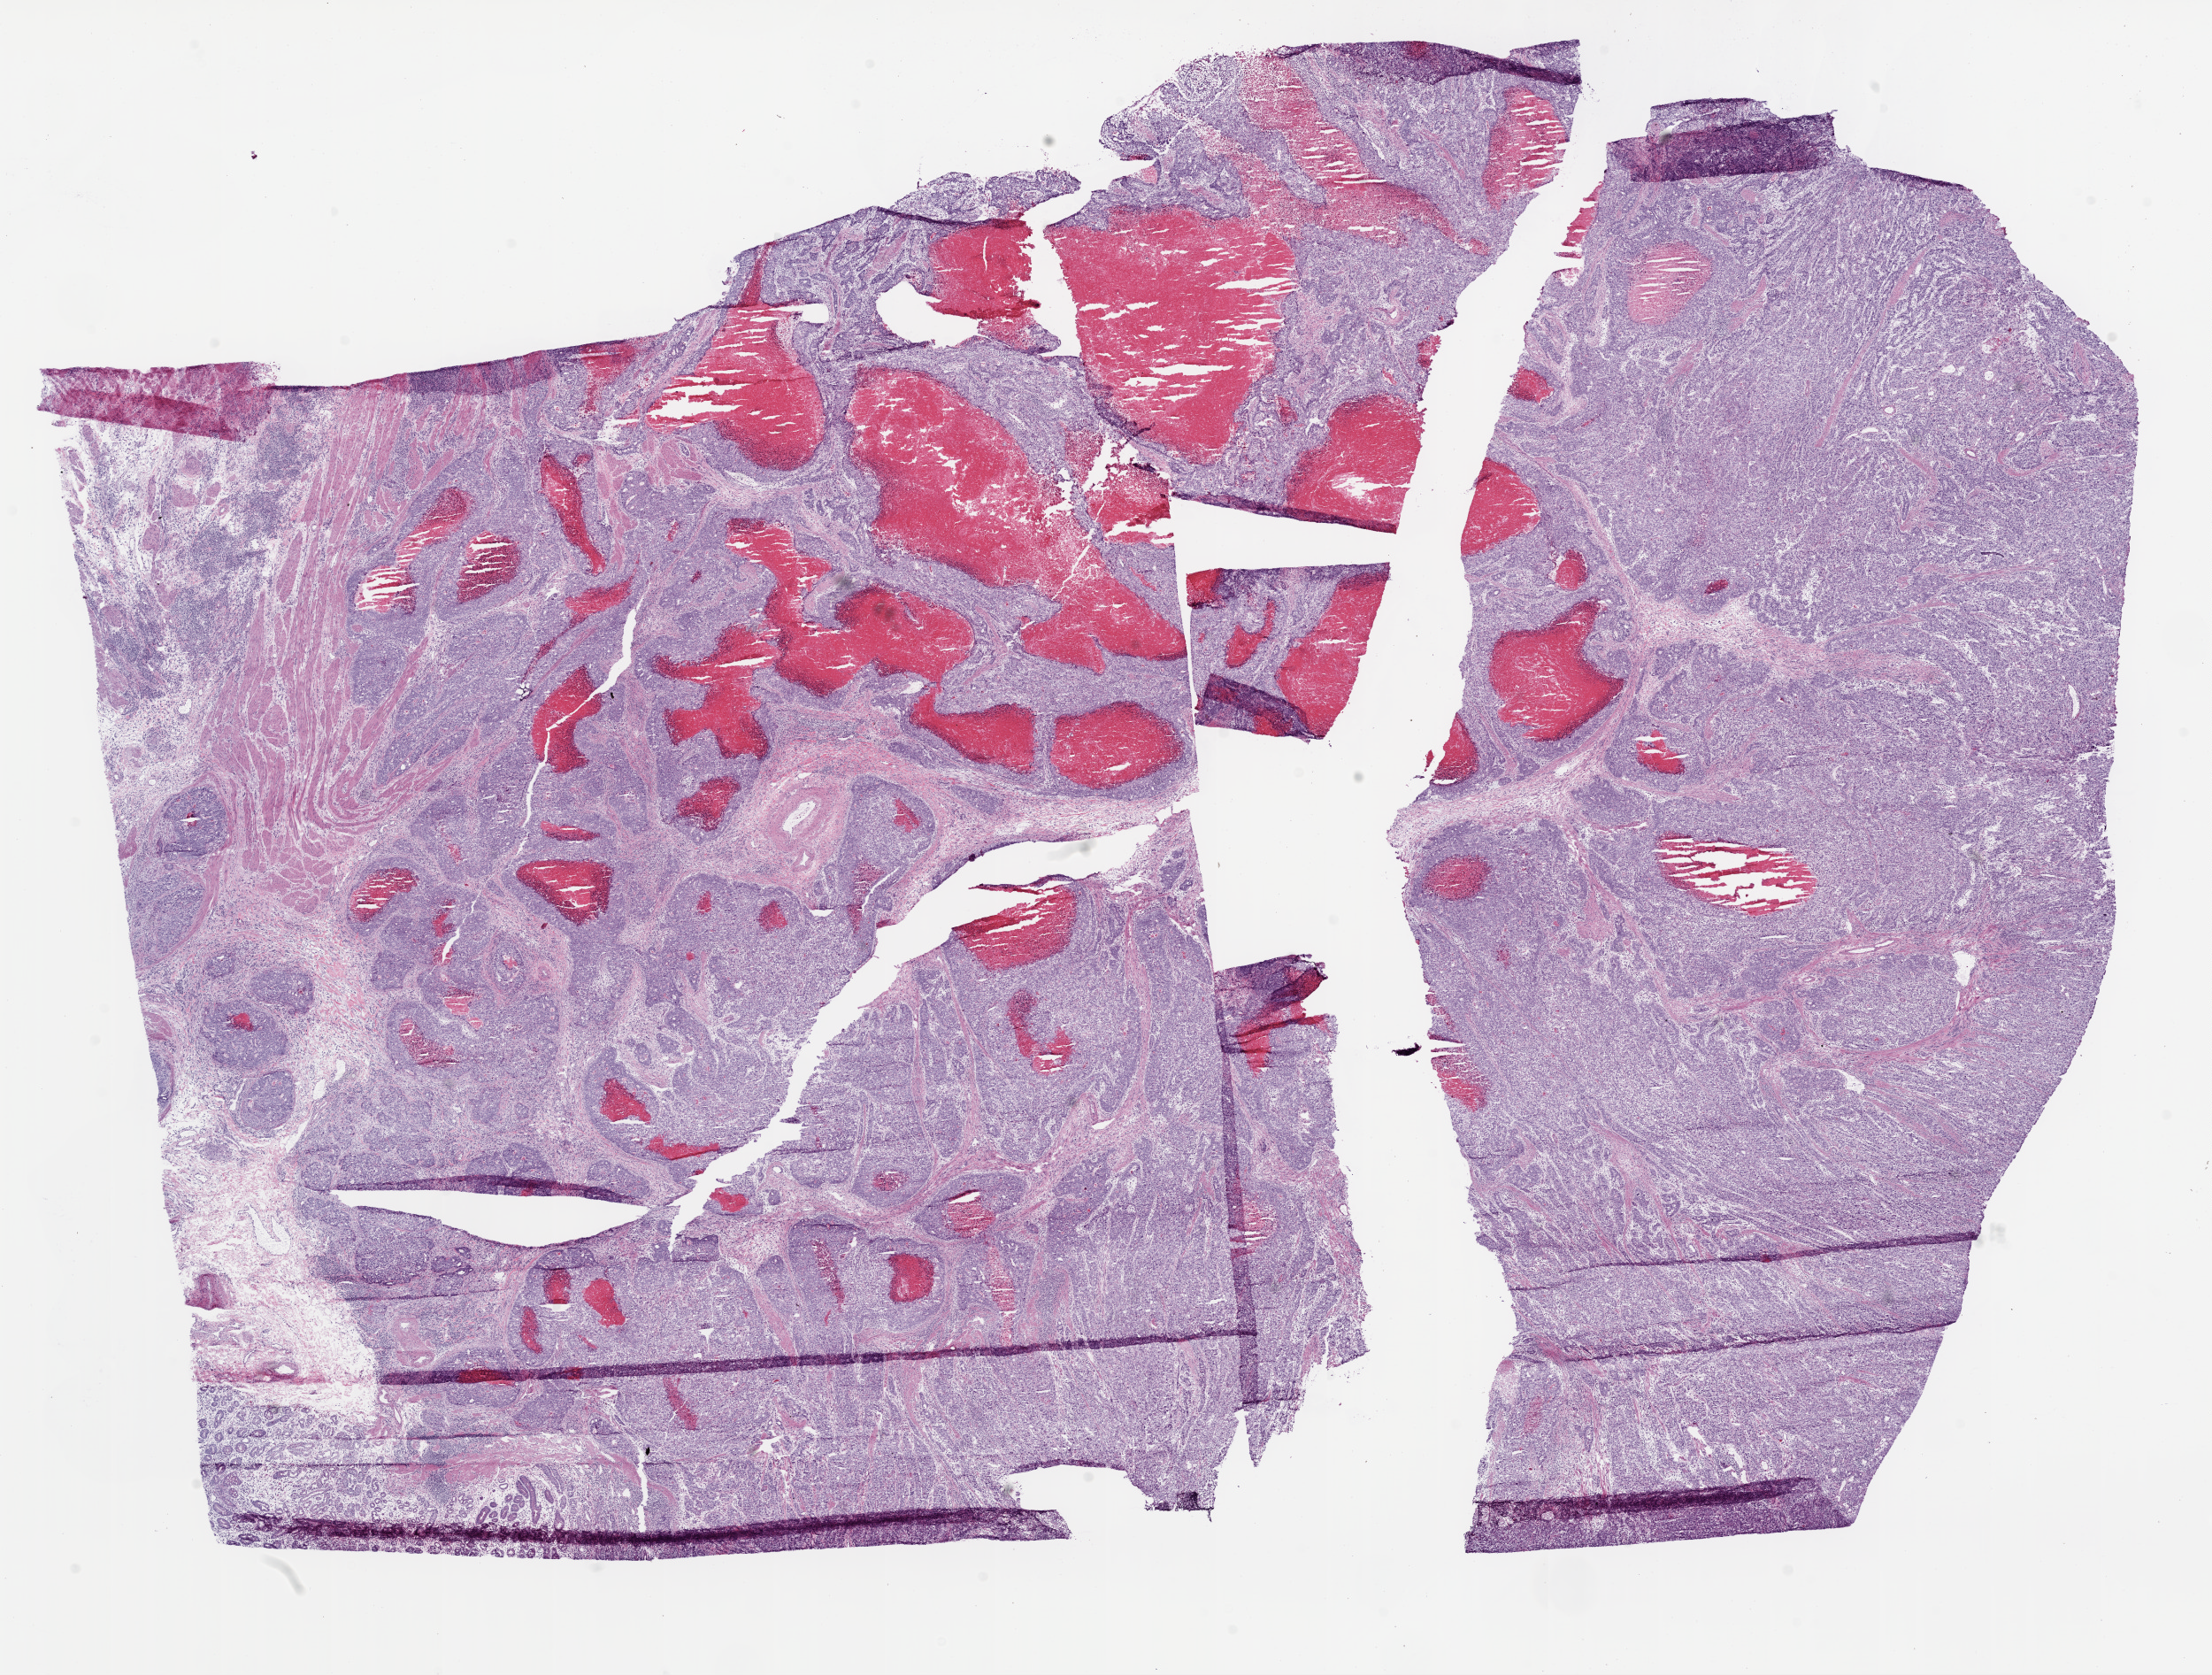
Digitized H&E-stained tissue section (whole slide), shown as a low-resolution overview of the whole scanned area (about 20.1 x 15.2 mm); frozen section from the bottom of the tissue portion; stomach, primary tumour sample. Male, age 75 years at initial diagnosis. Histologic grade: G3 (poorly differentiated). Pathologist review of this section (percent, as recorded): tumour cells 75%, tumour nuclei 75%, normal cells 5%, stromal cells 5%, necrosis 15%.
Histologic diagnosis: Adenocarcinoma, NOS (cardia, NOS).